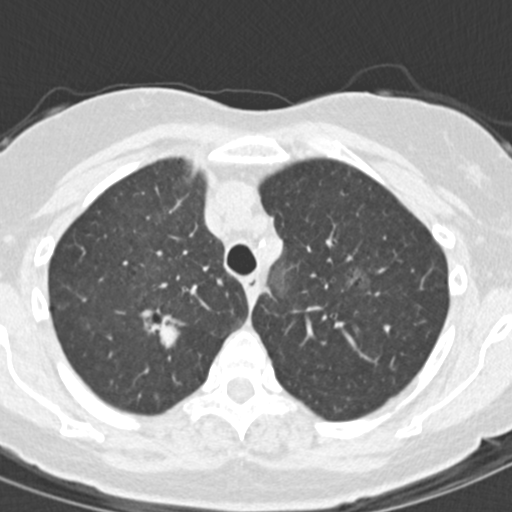
Low-dose screening chest CT, one axial slice; slice 118 of 157 in the series (ordered by position); reconstruction kernel B30f; lung window (W 1500 / L -600 HU); 2 mm slice thickness; 512 × 512 image matrix.
Structures marked on this image (outlined manually by an expert reader):
- lesion 1 (tumor, upper lobe of right lung): bounding box [x1, y1, x2, y2] px = [146, 322, 181, 358]